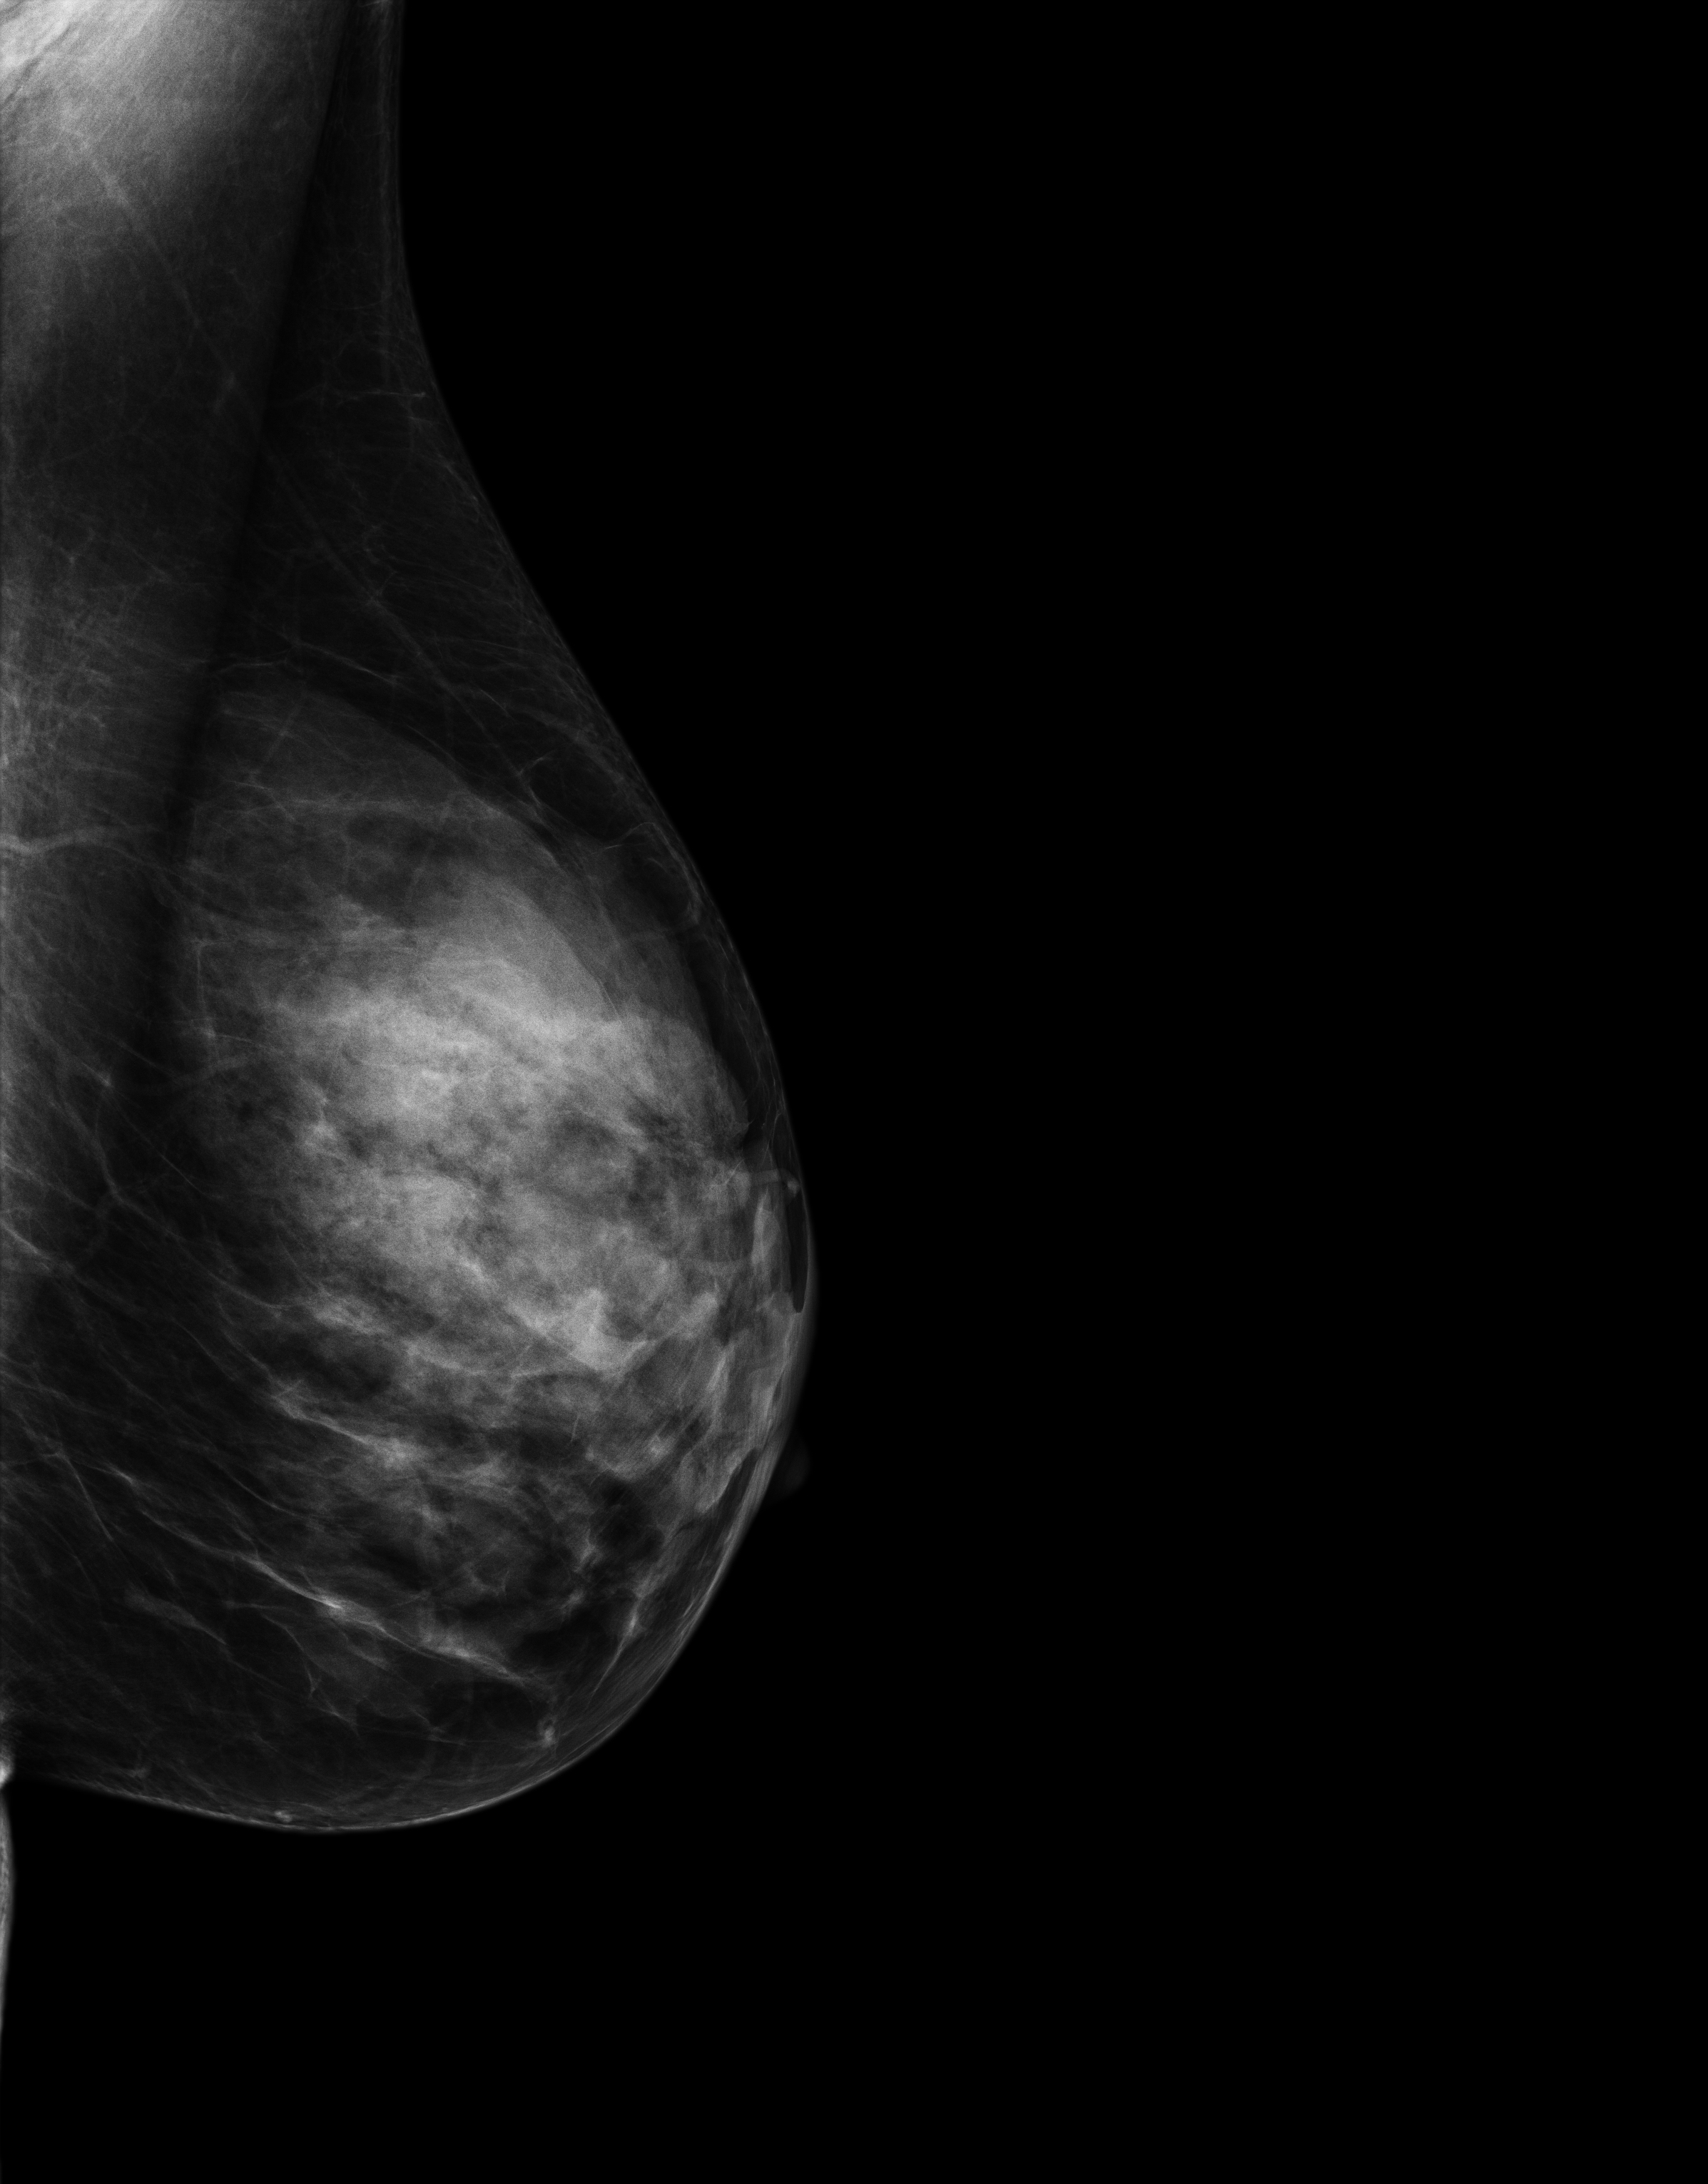
Full-field digital mammogram (FFDM), left breast, mediolateral oblique (MLO) view, screening examination, compressed breast thickness 50 mm. Female patient, age 60 years.
Breast density at the screening exam (both breasts): extremely dense (BI-RADS density category d). Final BI-RADS category for the screening round (tomosynthesis exam, both breasts): category 1. Recall: no recall after this screen.